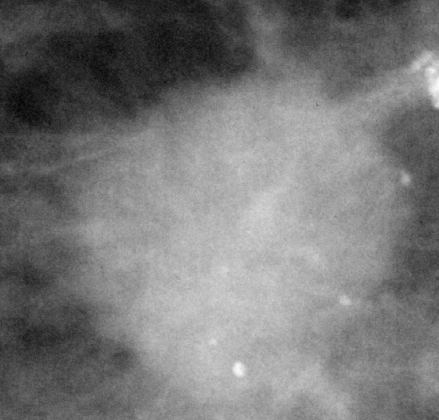
Region of interest cut from a scanned film mammogram (one marked finding); right breast; CC view.
Marked abnormality: mass, shape irregular, margins spiculated; BI-RADS assessment category 4; pathology (as recorded): malignant.